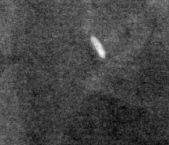
Crop from a digitized film mammogram around one marked abnormality, right breast, CC view, BI-RADS breast density category 1 (scale 1–4).
Finding: calcifications, distribution regional; BI-RADS assessment category 2; benign; no additional work-up was recommended (benign without callback).